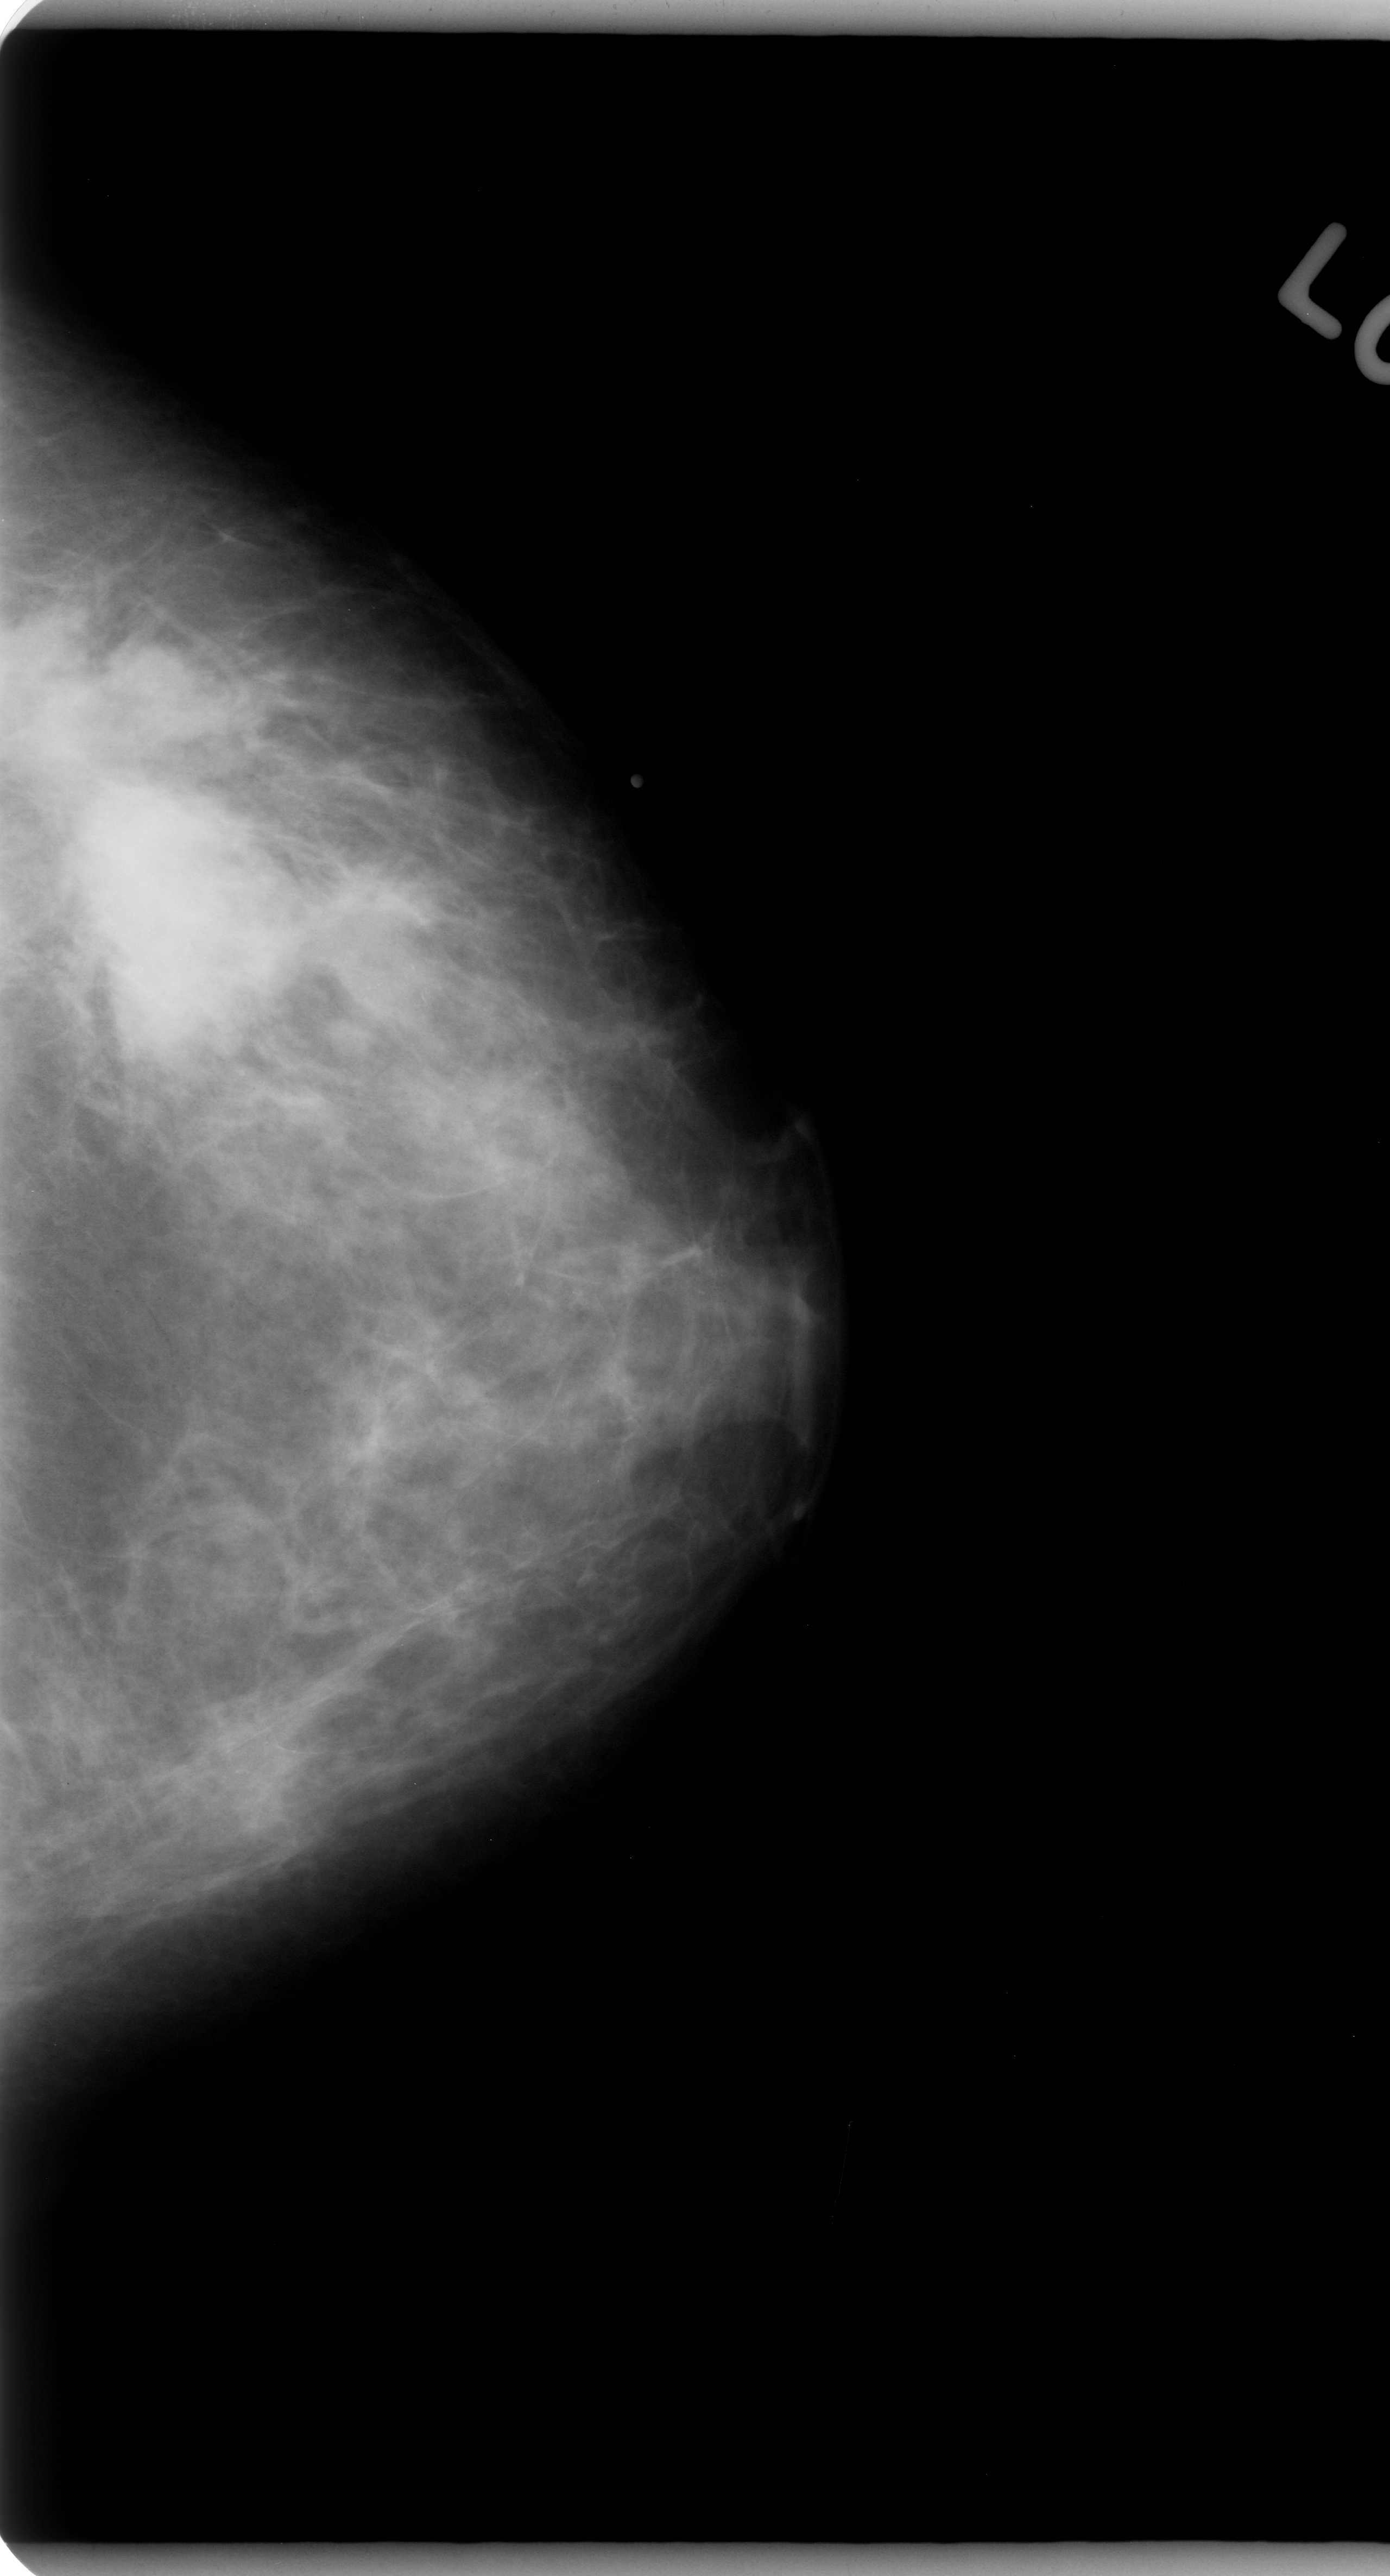
Mammogram (digitized film); left breast; CC view; breast composition: scattered fibroglandular densities (BI-RADS density category 2 of 4); 1390 × 2576 image matrix.
Expert-marked regions of interest on this film, with their recorded descriptors:
- mass, shape irregular, margins ill defined; BI-RADS assessment category 5; subtlety rating 5 on a 1 (subtle) to 5 (obvious) scale; pathology (as recorded): malignant: bounding box [x1, y1, x2, y2] px = [0, 755, 387, 1128]